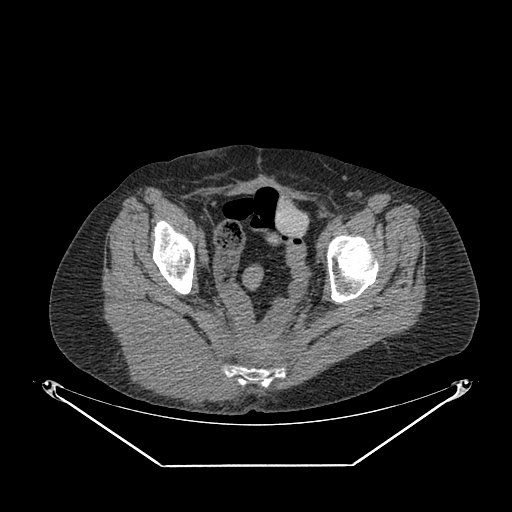
CT of an extremity soft-tissue mass (from a PET/CT study), one axial slice; slice 61 of 267 in the series (ordered by position); reconstruction kernel SOFT; 140 kVp; soft-tissue window (W 400 / L 40 HU); 3.75 mm slice thickness; 512 × 512 image matrix. Female patient. From the clinical record (not read from this slice): histological type: spindle cell suggestive of myxofibrosarcoma; grade: intermediate; site of the primary tumour: right buttock.
Annotated regions visible in this slice (expert contour drawn on MRI and transferred to this co-registered scan by the dataset authors):
- gross tumour volume (mass): bounding box <116,317,234,401> (left, top, right, bottom; pixels)